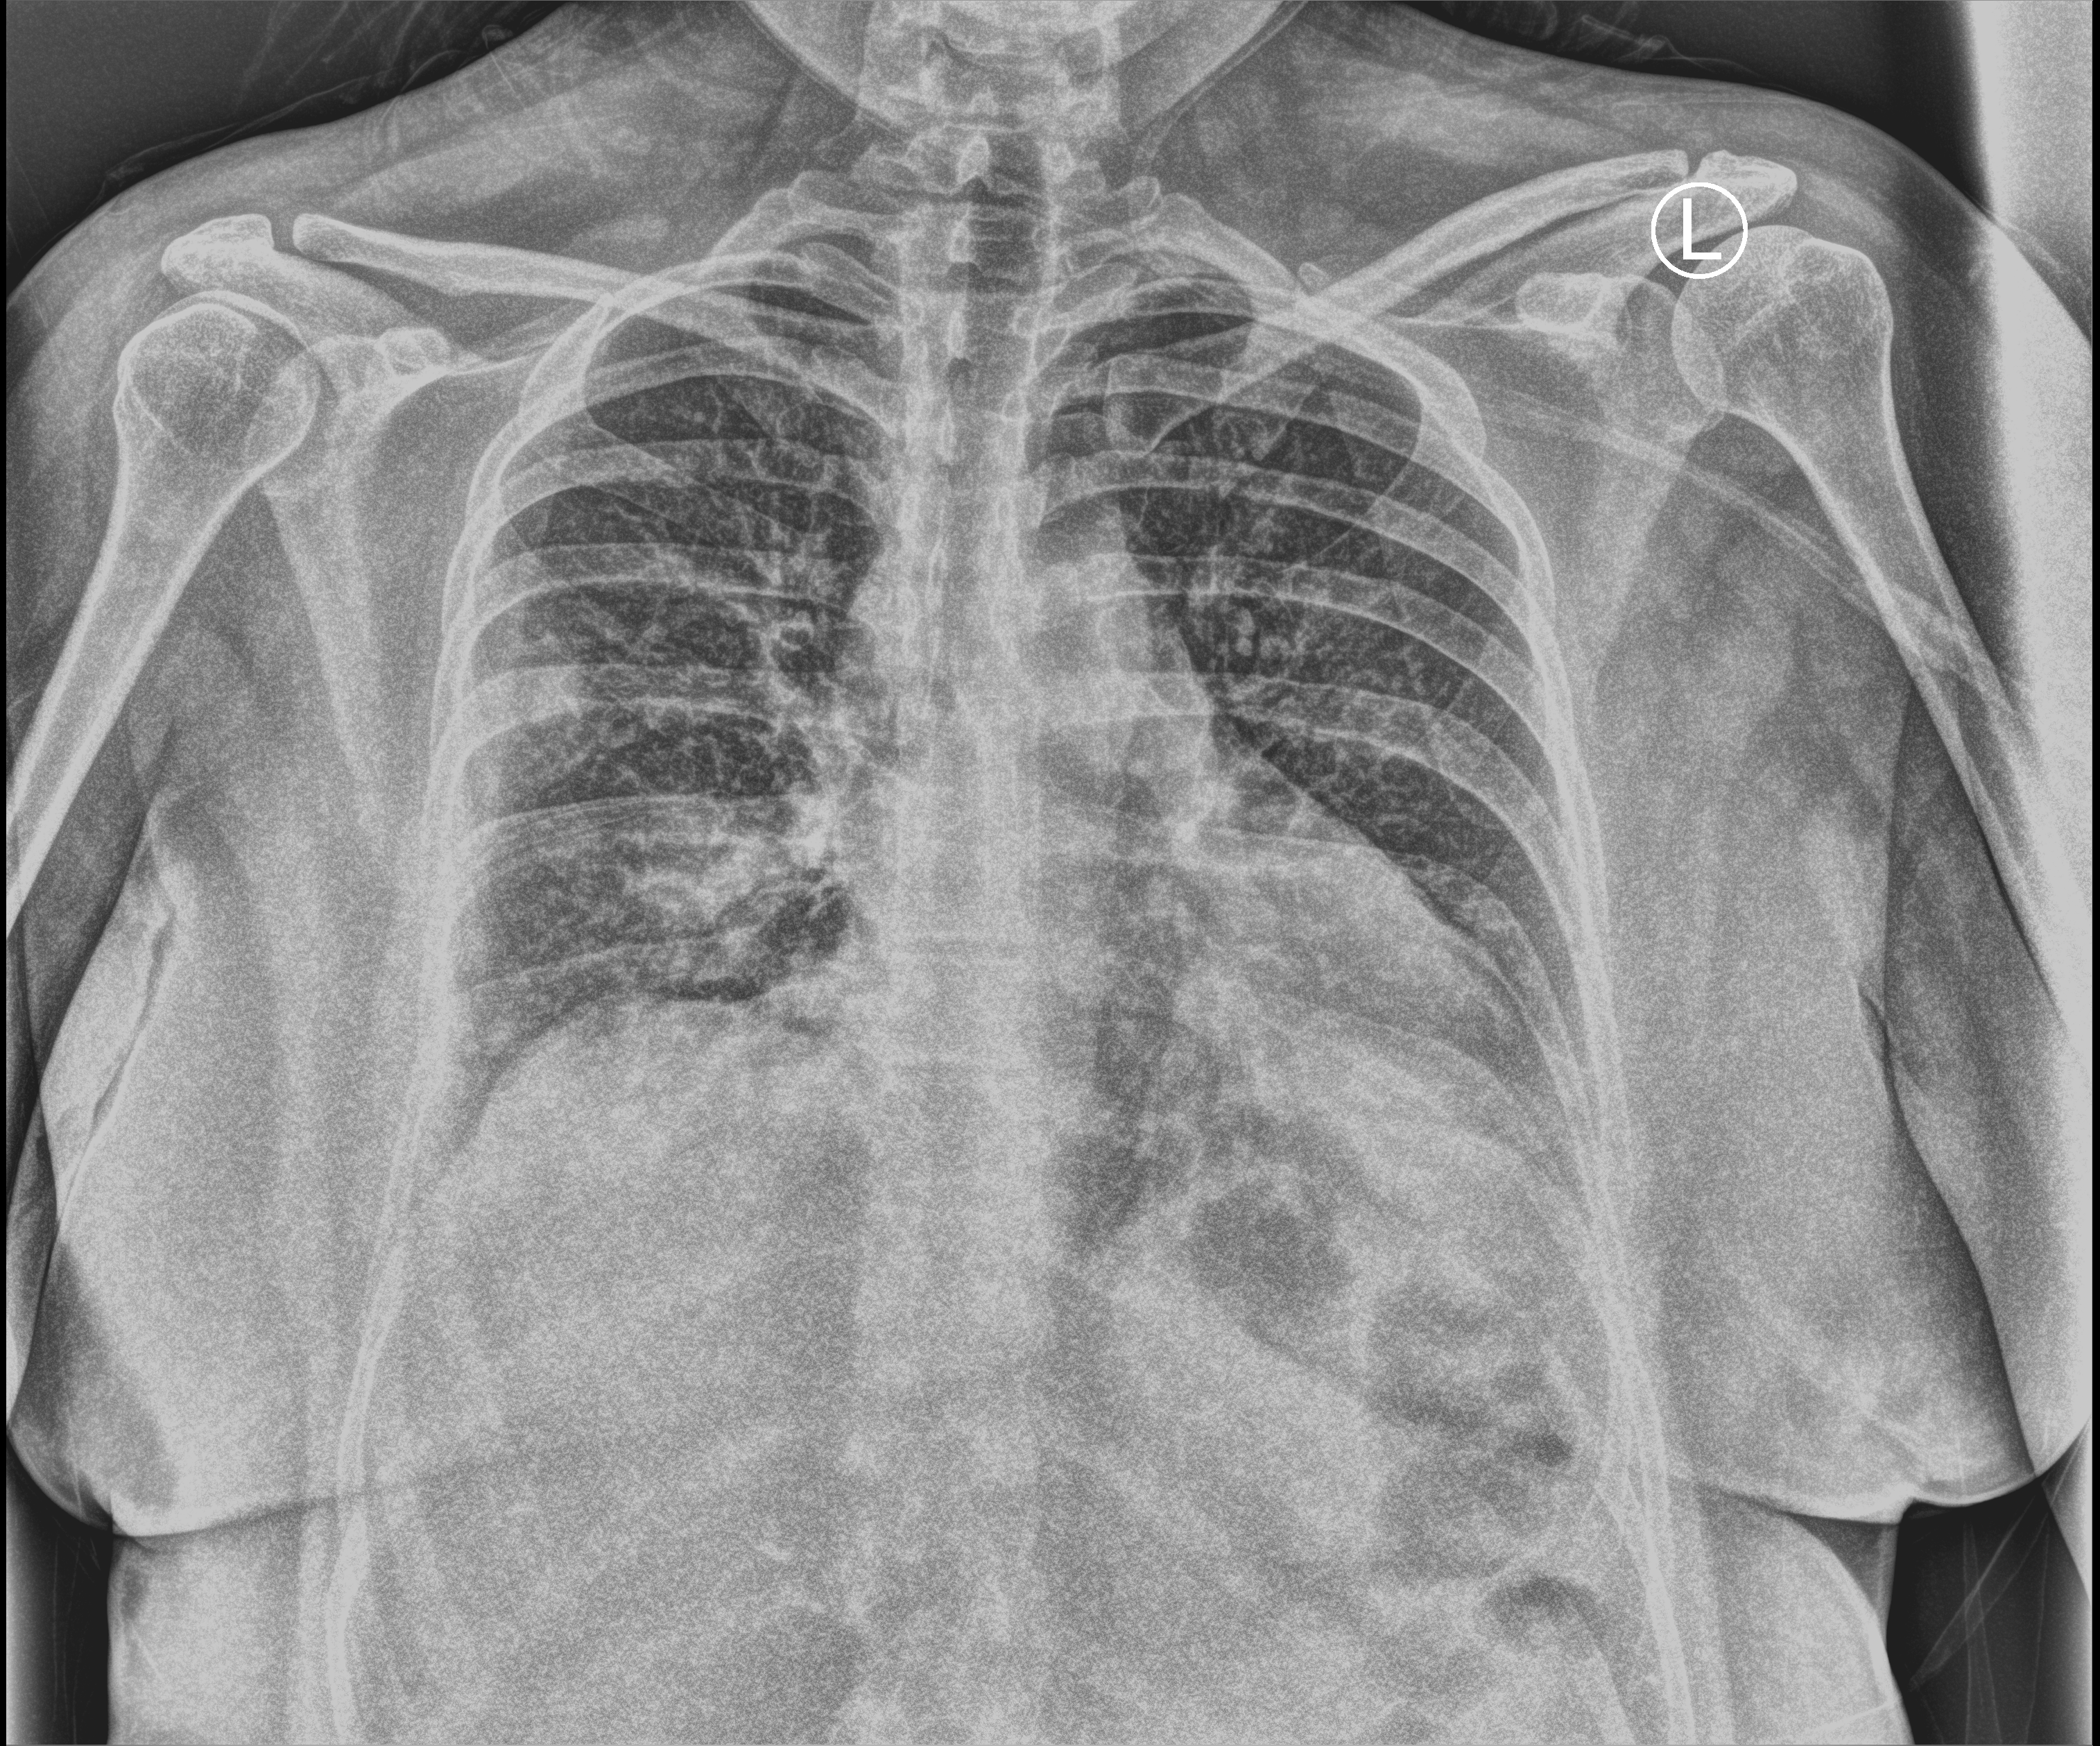
Portable chest radiograph. Female patient hospitalised with COVID-19, age 18–59 years.
Hospital-stay facts (about this admission, not read from this image; timing relative to this image not recorded):
- diabetes (admission record): no
- admitted to intensive care during this hospital stay: no
- length of hospital stay: 1 day